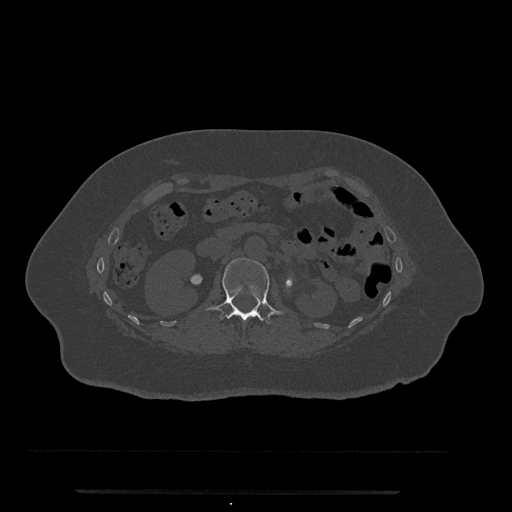
CT including the spine, one axial slice. Slice 104 of 797 in the series (ordered by position). Reconstruction kernel Br40s/3. Bone window (W 1800 / L 400 HU). 0.5 mm slice thickness. 512 × 512 image matrix, field of view 440 × 440 mm. Patient: female, 51 years. Case-level facts recorded for this patient, not image findings: primary cancer: neuro; vertebrae with lytic lesions (as recorded): T8.
Structures marked on this image (semi-automatic segmentation, software-assisted and operator-edited):
- L1 vertebra: bounding box [x1, y1, x2, y2] px = [205, 258, 284, 324]